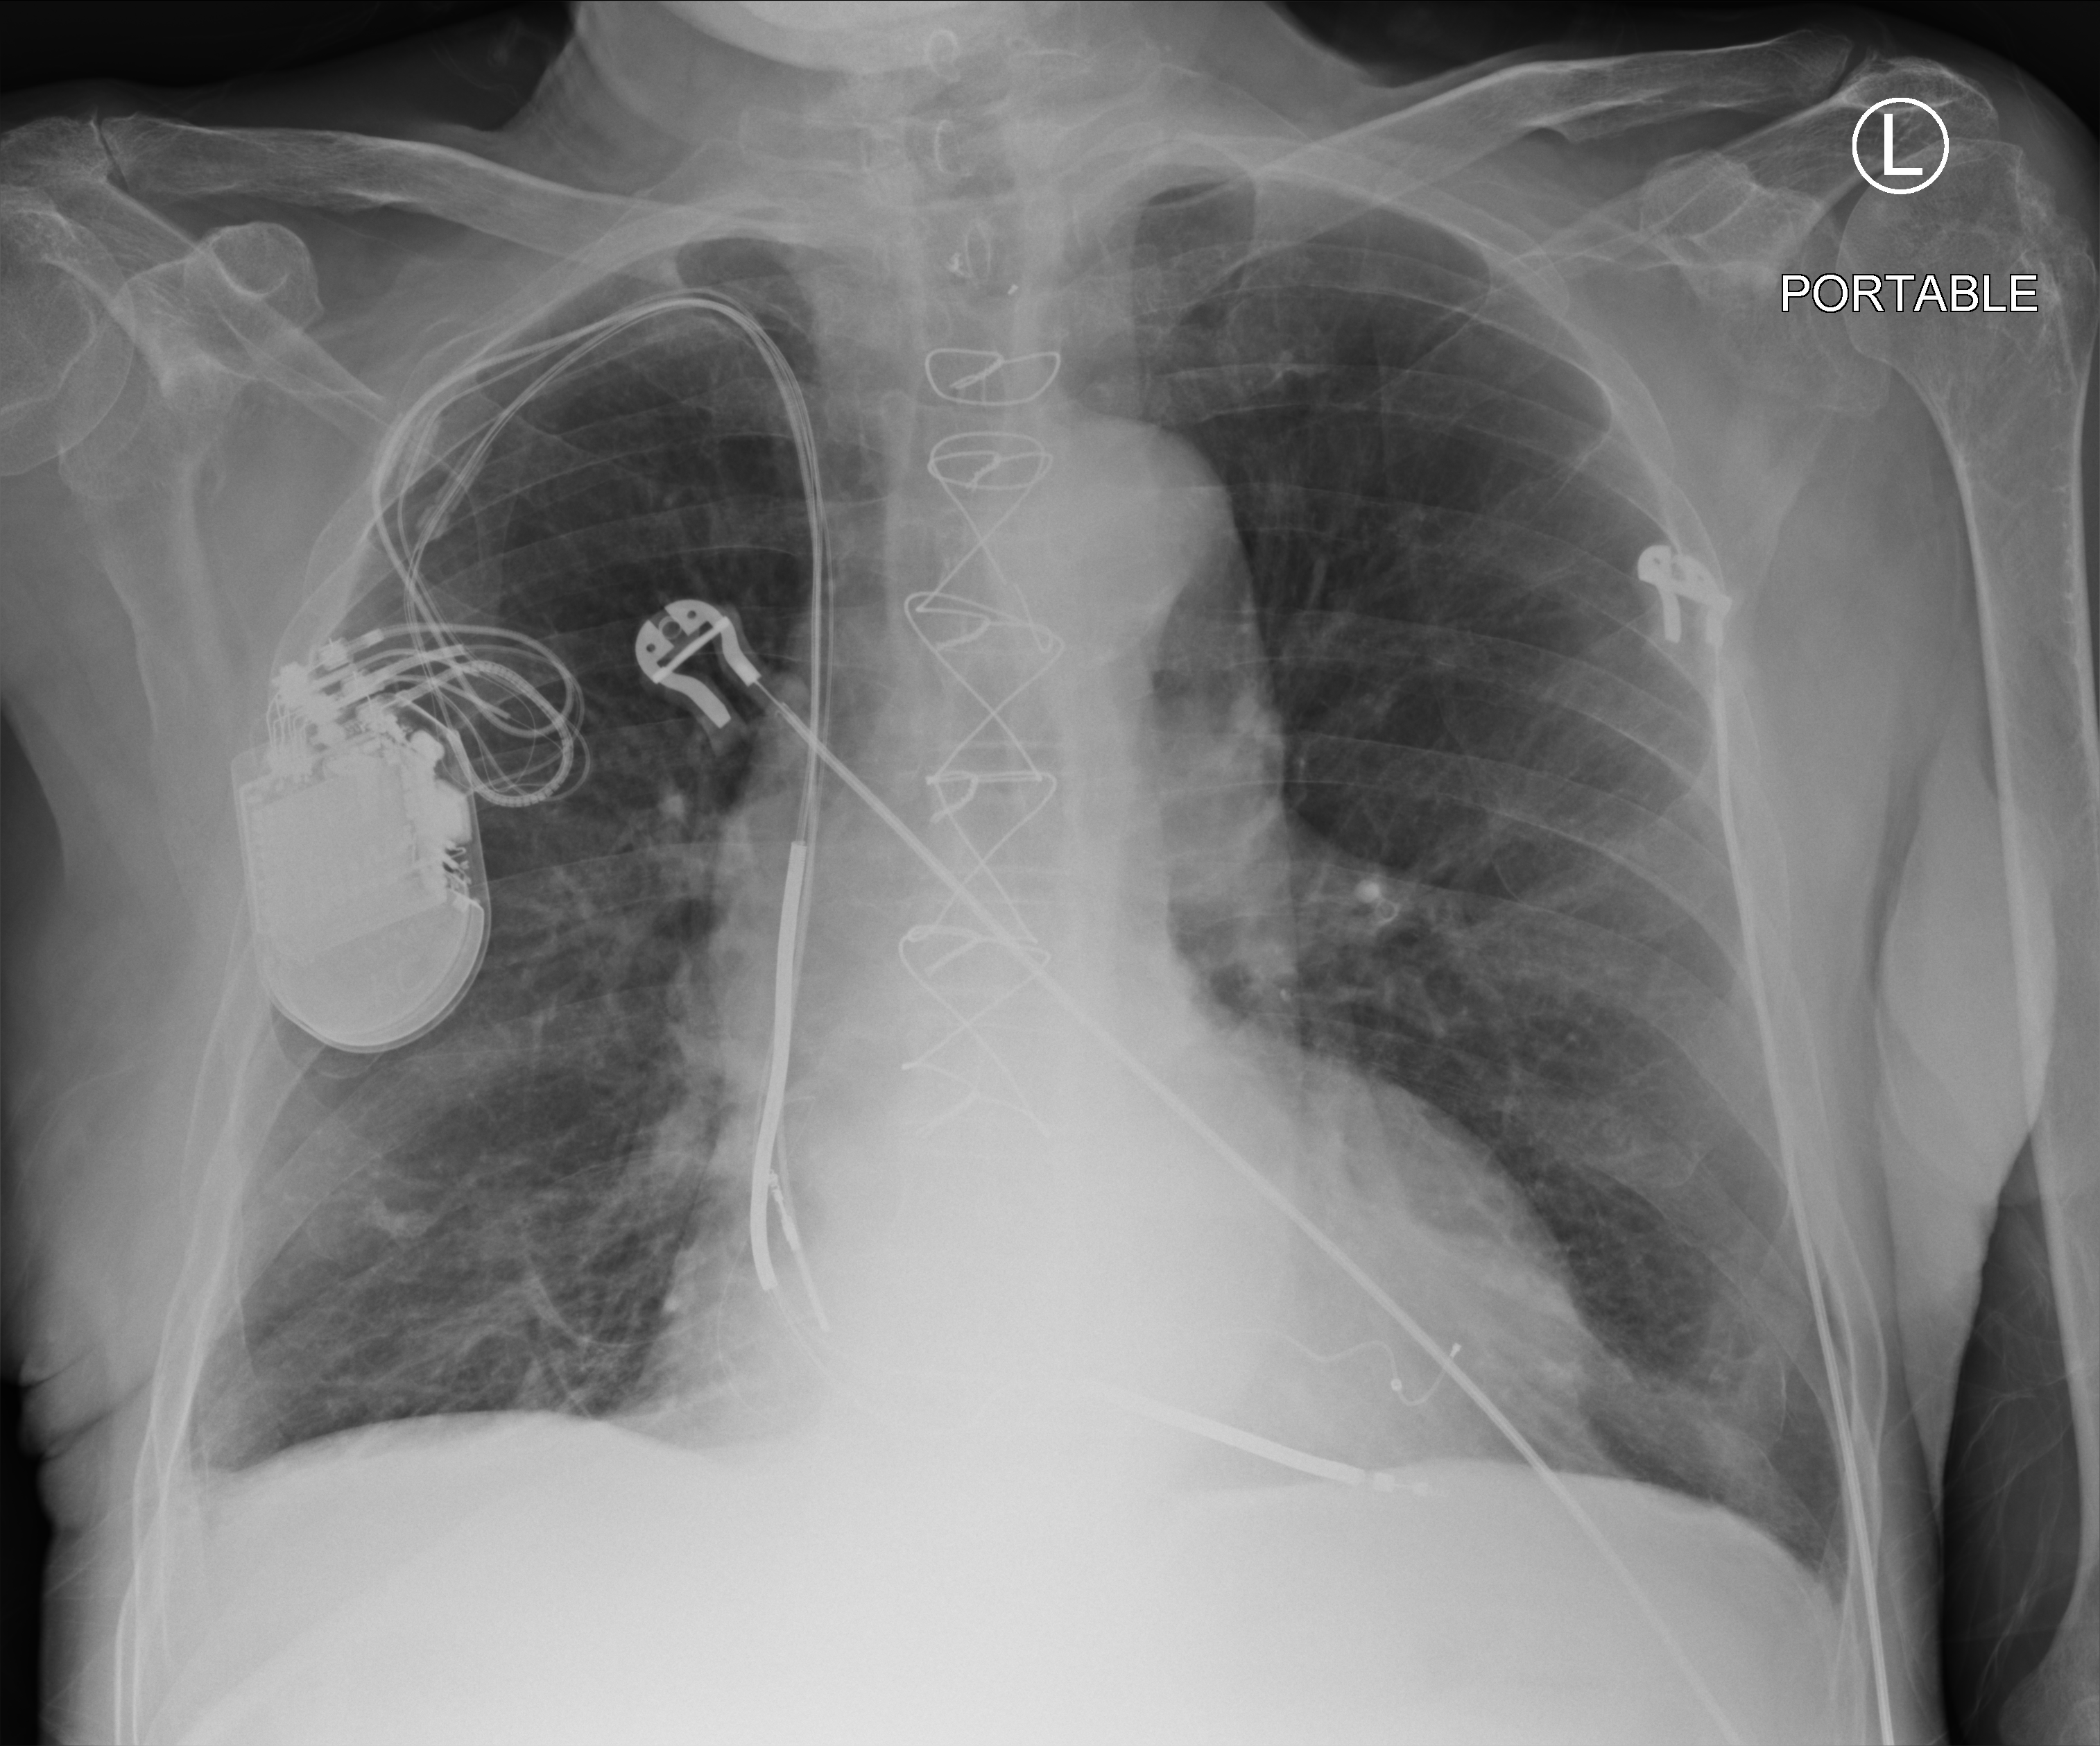
Portable chest radiograph, anteroposterior (AP) projection. Male patient hospitalised with COVID-19, age 75–90 years.
Admission-level facts for this patient (not findings on this image; timing relative to this image not recorded): mechanically ventilated during this hospital stay: no.